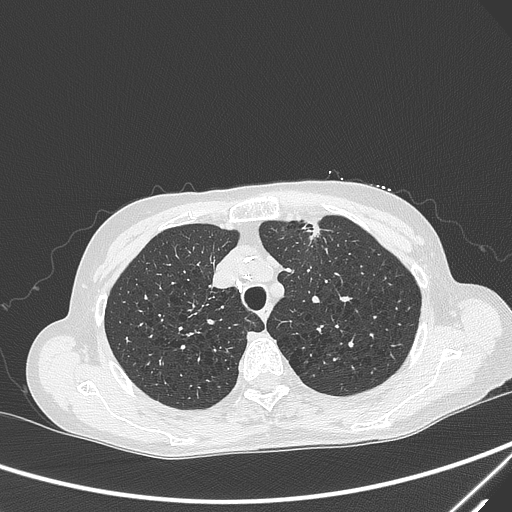
Chest CT, one axial slice. 120 kVp. Lung window (W 1500 / L -600 HU). 1 mm slice thickness. 512 × 512 image matrix, field of view 350 × 350 mm. Patient: female, 71 years. From the clinical record (not read from this slice): clinical TNM (as recorded): T1c N0 M0; histopathological grade: G2-3.
Annotated regions visible in this slice (bounding box drawn by a radiologist):
- lung tumour (recorded histology: adenocarcinoma): bounding box <294,215,331,250> (left, top, right, bottom; pixels)